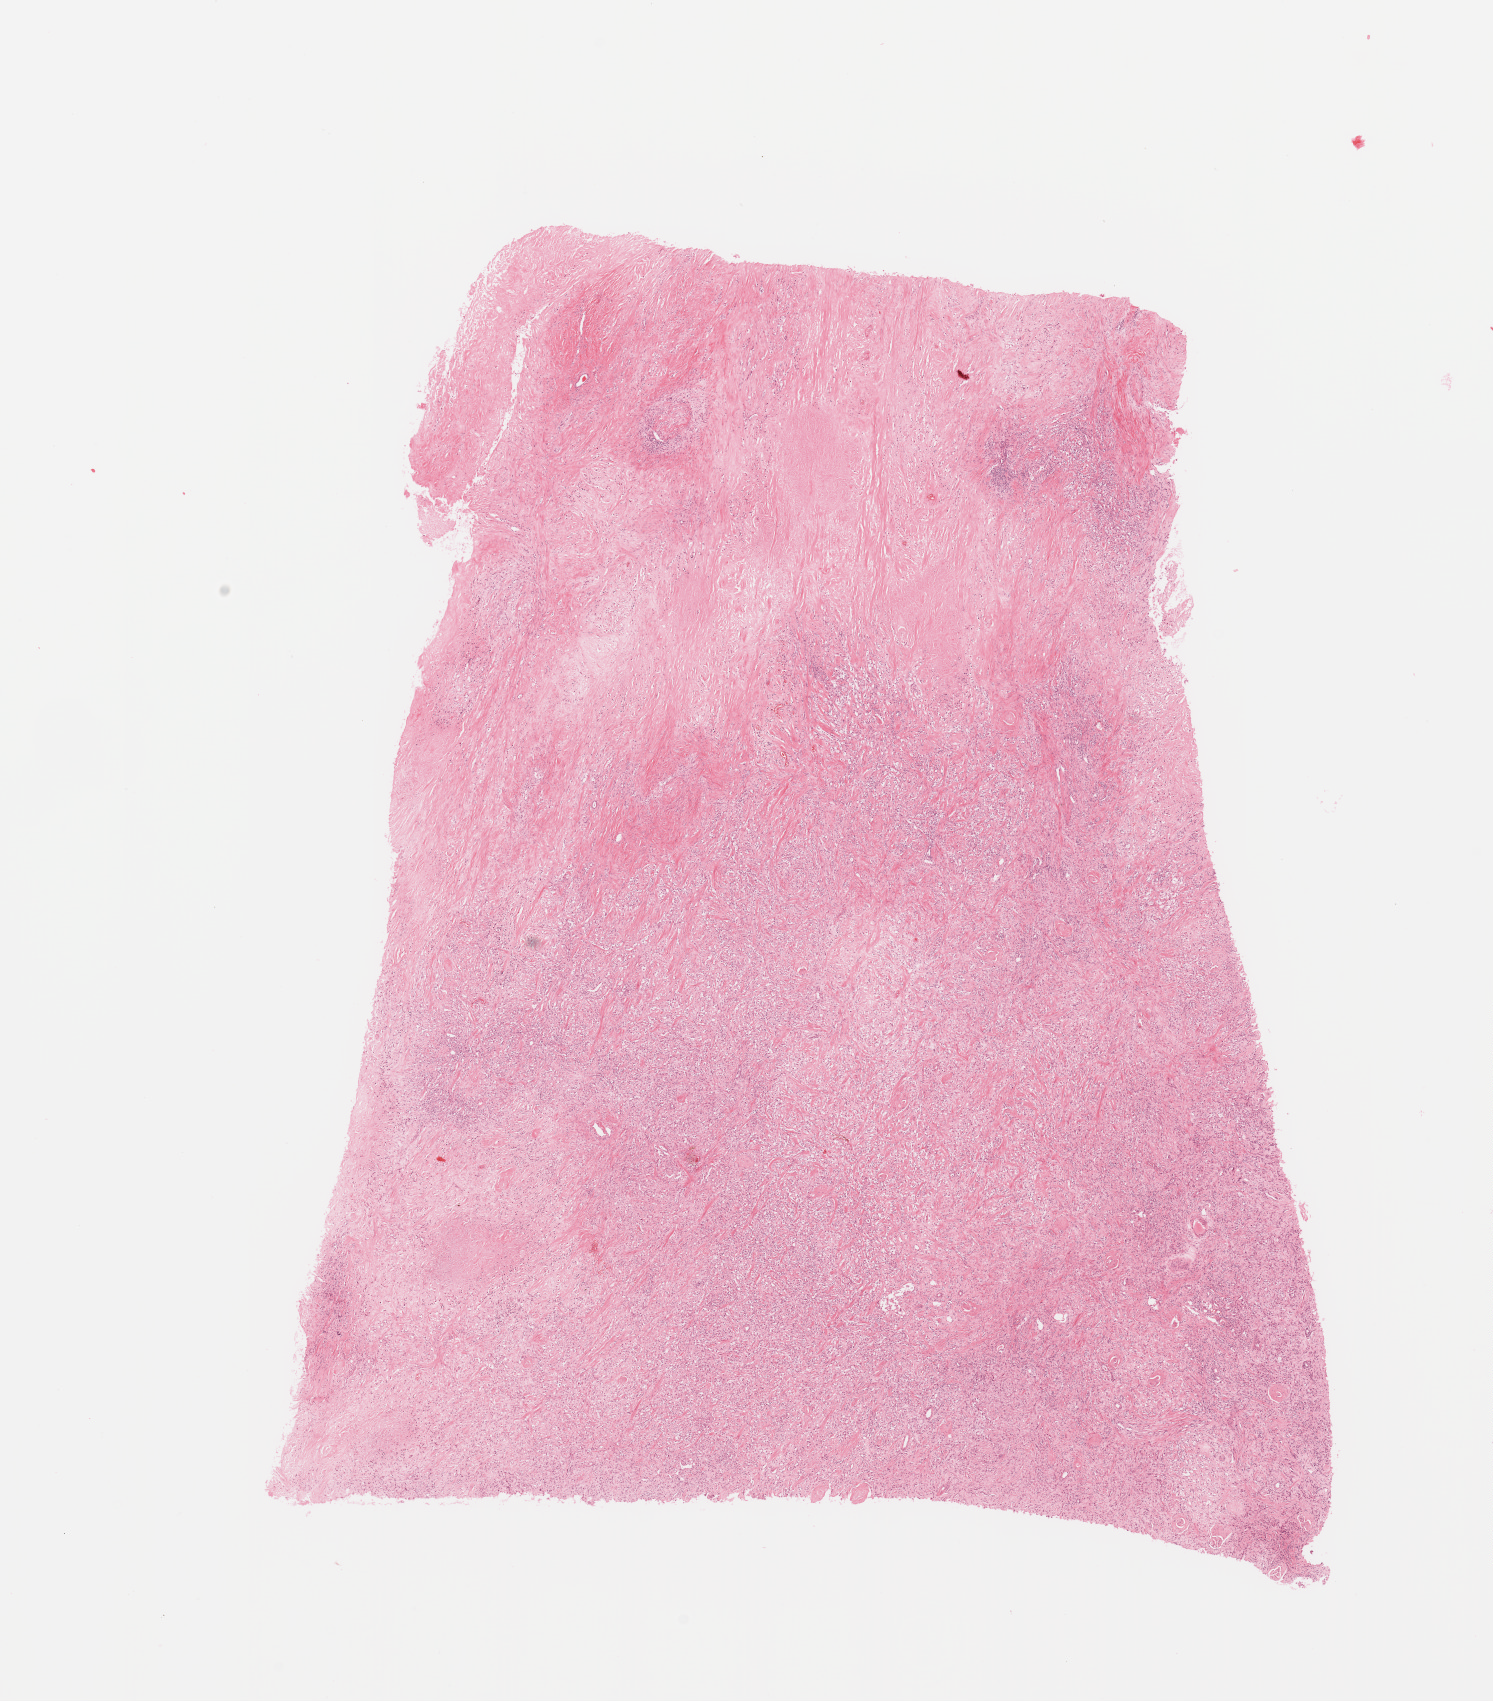
Hematoxylin and eosin (H&E) stained whole-slide image, low-resolution overview of the scanned area, about 11.8 x 13.5 mm (slide scanned at 20x); tumour tissue sample, sampled site: kidney. Female, 68 y/o. Histologic grade: G3 (poorly differentiated). Composition of this section per pathologist review: tumour nuclei 80%, necrosis 10%.
AJCC pathologic stage: IV. Diagnosis: Renal cell carcinoma, NOS.